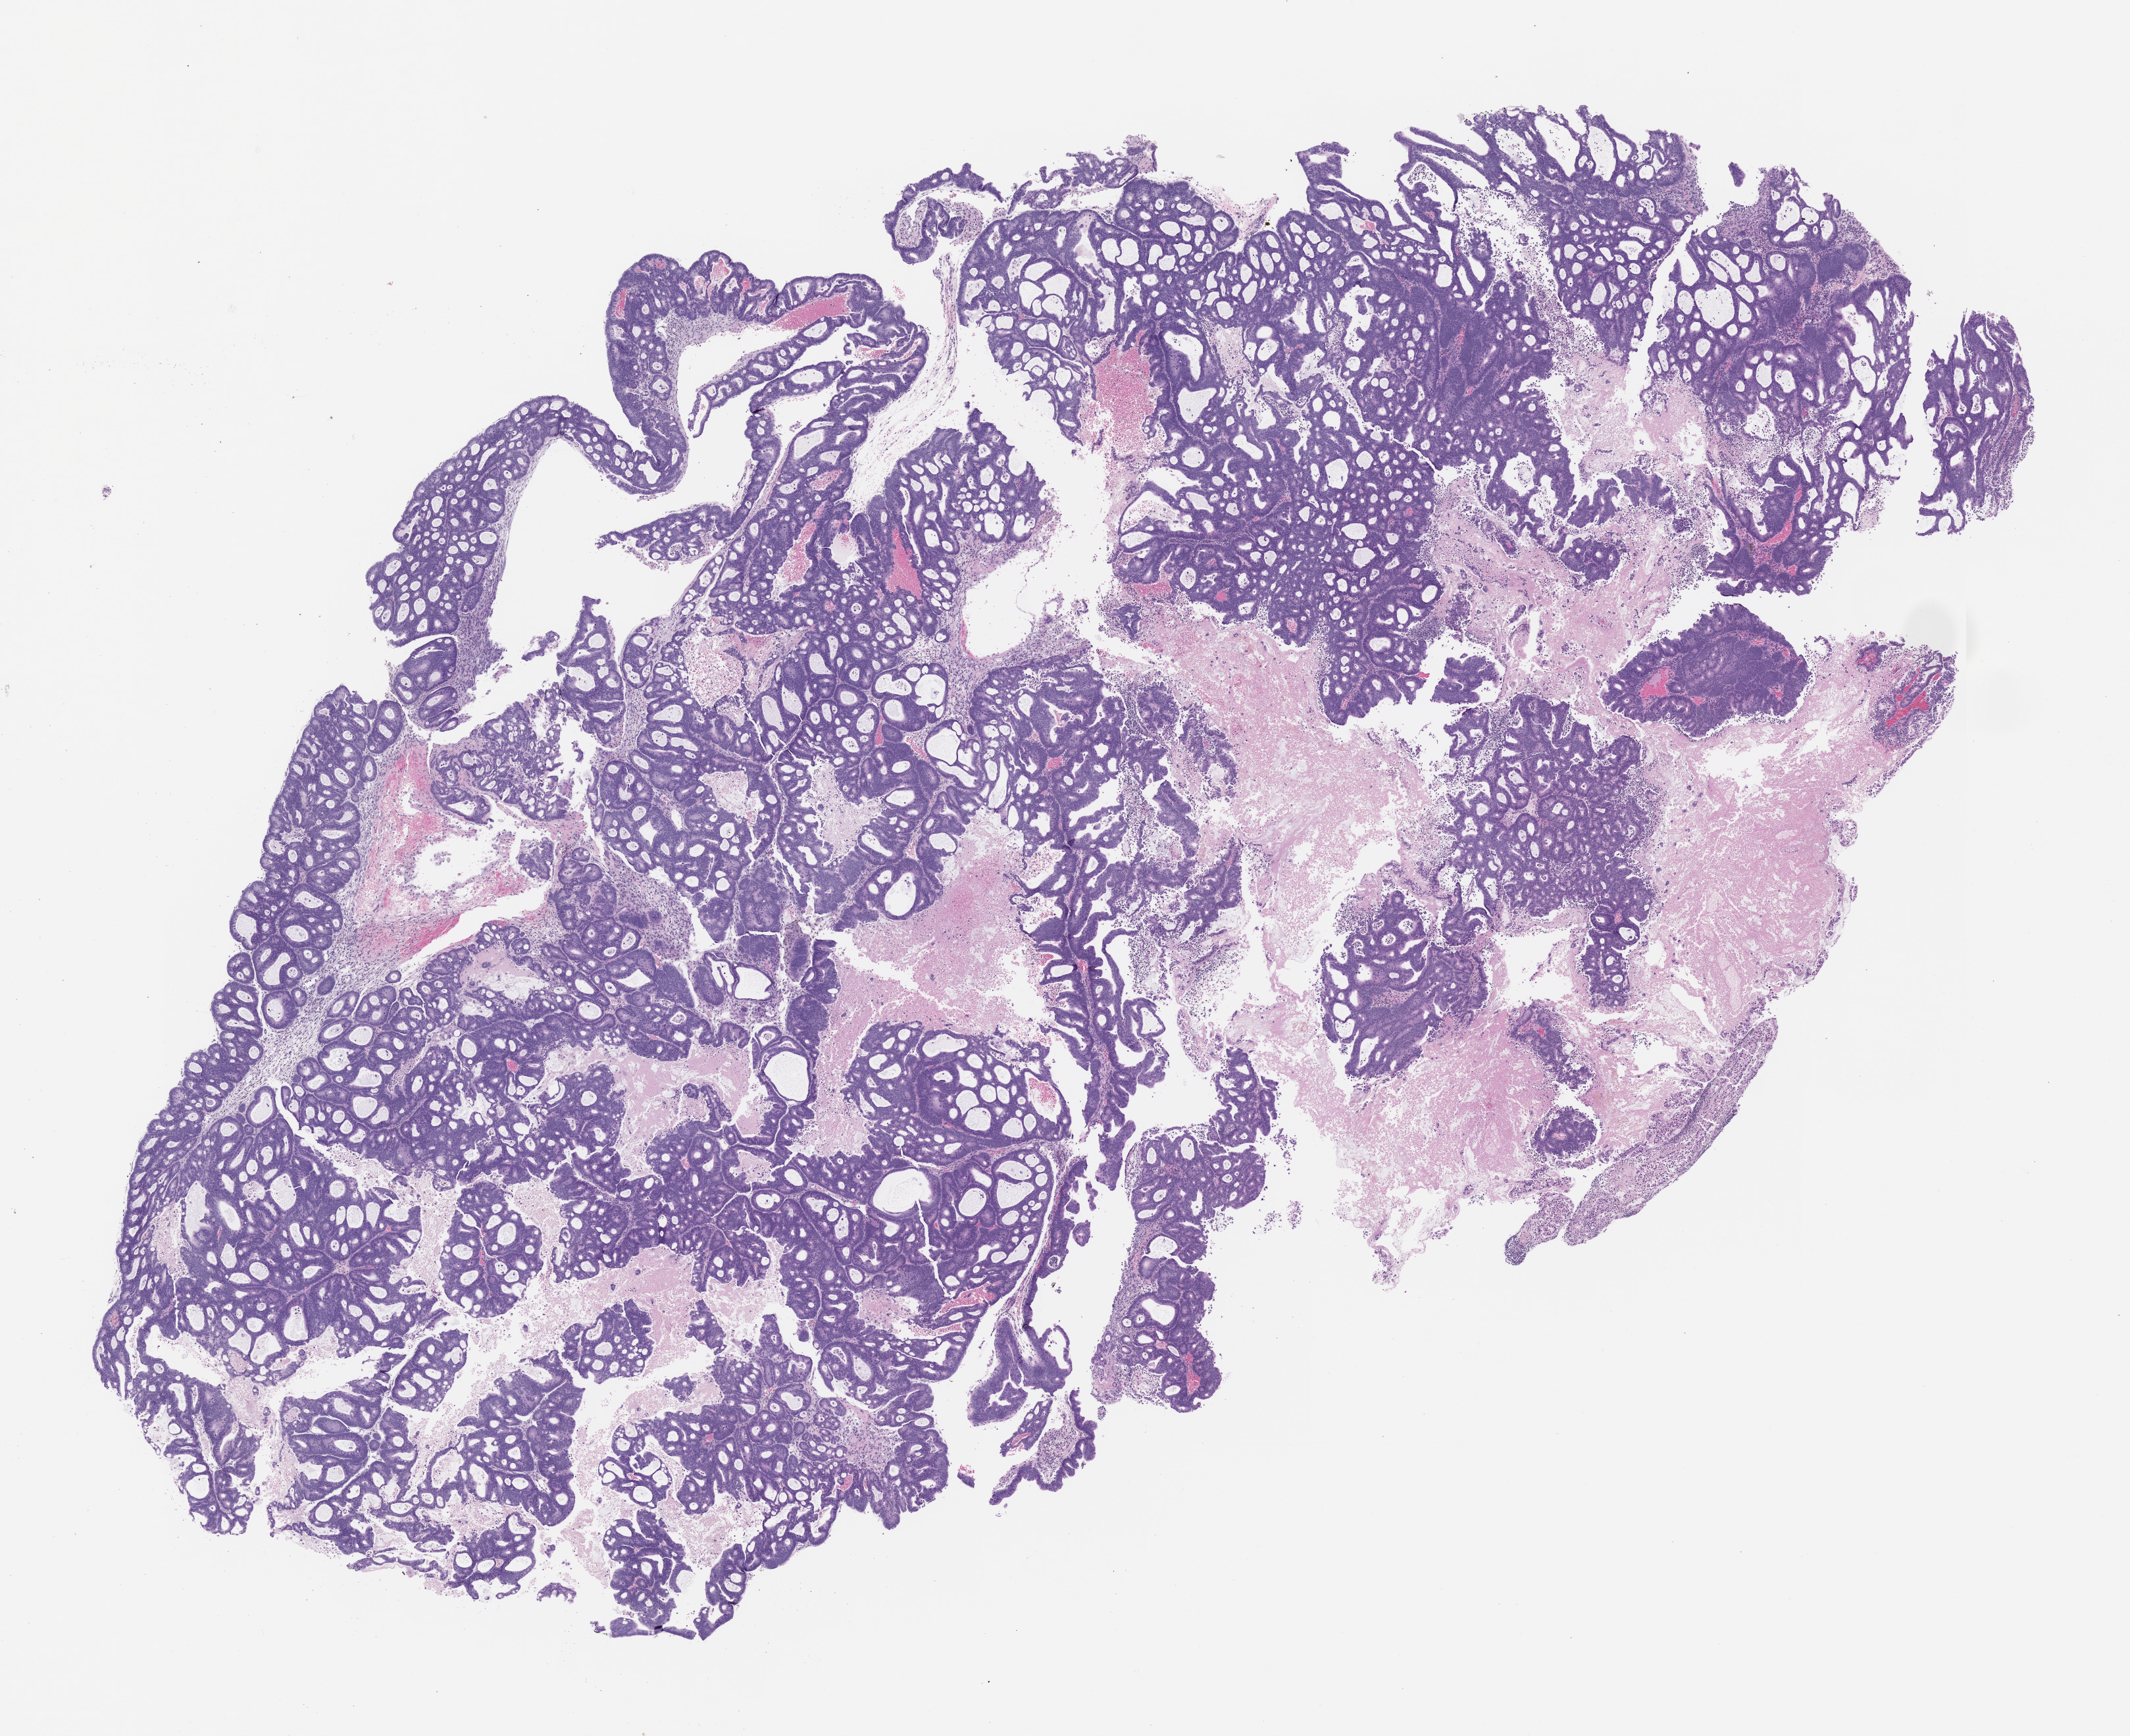
Whole-slide image, haematoxylin and eosin: patient-derived xenograft (human tumor grown in a mouse), passage 3, low-resolution overview of the scanned area, about 13.0 x 10.6 mm, FFPE section, originating tumor site category: colon.
Originating patient diagnosis: Colon Adenocarcinoma.